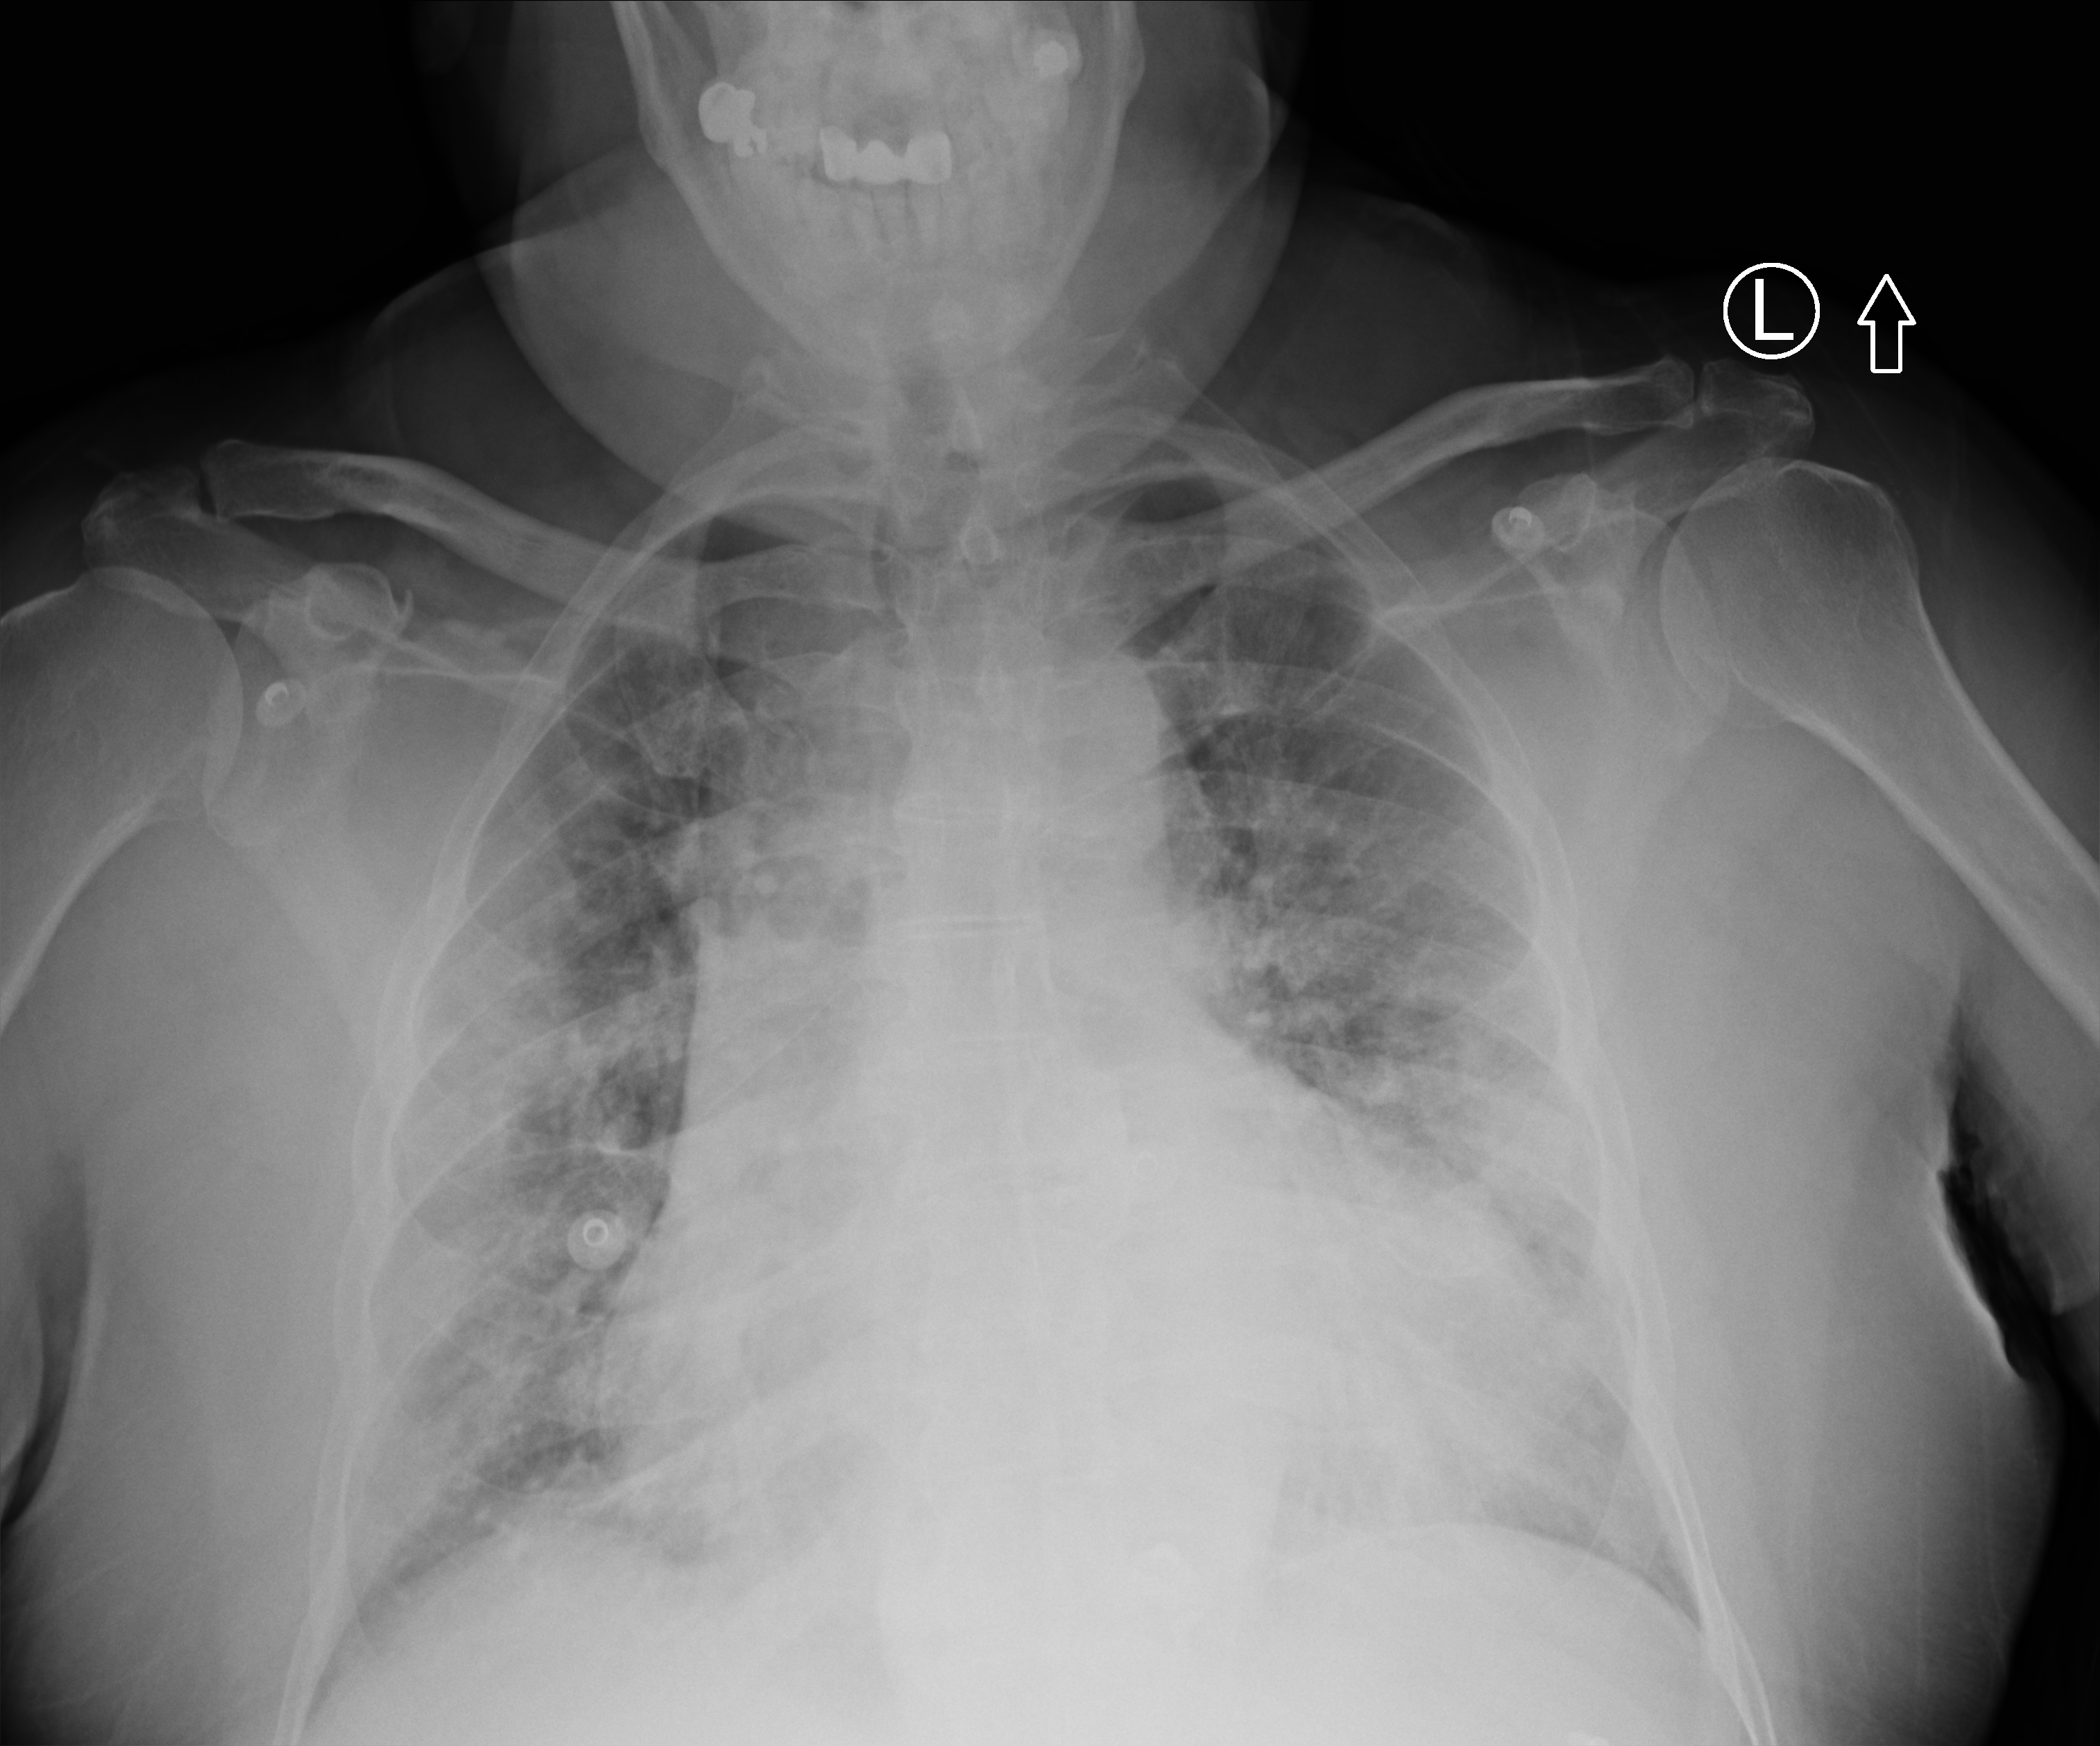
Chest X-ray (portable). Male patient hospitalised with COVID-19, age 60–74 years.
From the hospital-stay record, not from the radiograph (when in the stay this image was taken is not recorded):
- admitted to intensive care during this hospital stay: yes
- mechanically ventilated during this hospital stay: yes